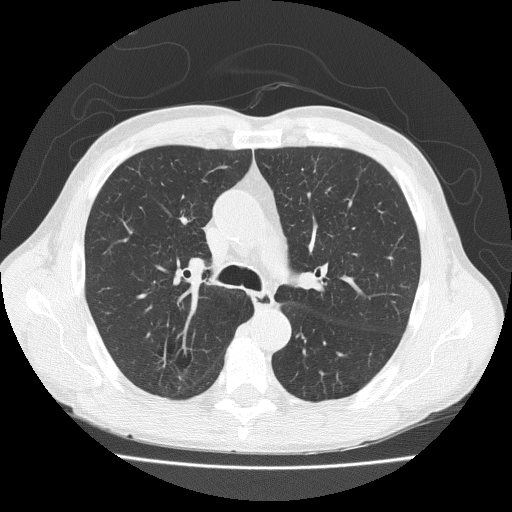
Axial slice from a low-dose chest CT screening exam; baseline screening round; lung window (W 1500 / L -600 HU); 2 mm slice thickness; lung (sharp) reconstruction kernel (FC51). Male participant, aged 73 years at enrolment. Current smoker at enrolment.
Expert reader's lesion annotation, bounding box <145,336,196,383> (left, top, right, bottom; pixels). No non-calcified nodule or mass ≥4 mm was recorded by the screening reader at this exam. Participant outcome: lung cancer diagnosed 777 days after this screen — adenosquamous carcinoma, right upper lobe, well differentiated (G1), stage IA (AJCC 6th edition), 20 mm at pathology.